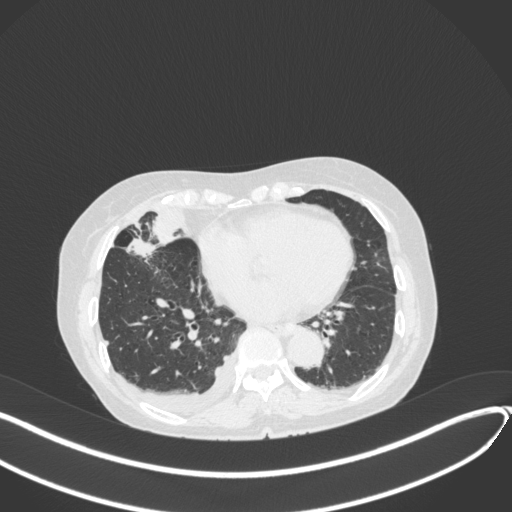
Chest CT, one axial slice; slice 144 of 418 in the series (ordered by position); 120 kVp; lung window (W 1500 / L -600 HU); 1 mm slice thickness; 512 × 512 image matrix, field of view 400 × 400 mm. Female patient, age 75 years. From the clinical record (not read from this slice): clinical TNM (as recorded): T2a N3 M0.
Outlined on this slice (rectangle marked by the reading radiologist):
- lung tumour (recorded histology: adenocarcinoma): bounding box [x1, y1, x2, y2] px = [123, 233, 157, 258]